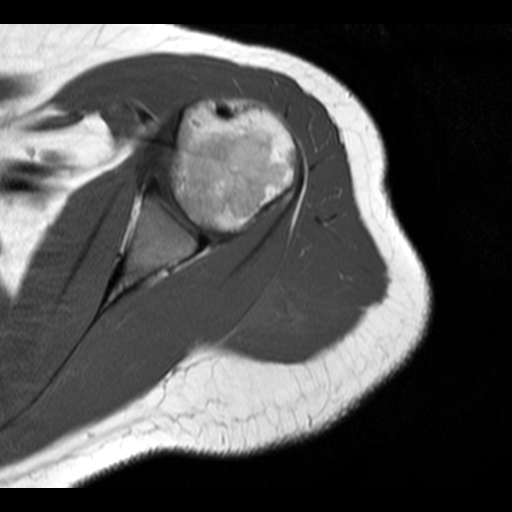
MRI of an extremity soft-tissue mass, one axial slice. Position 12 of 20 along the scan axis. 4 mm slice thickness. 512 × 512 image matrix, field of view 150 × 150 mm. Female patient. Case-level facts recorded for this patient, not image findings: histological type: malignant fibrous histiocytoma; grade: low; site of the primary tumour: left arm.
Structures marked on this image (expert manual segmentation):
- gross tumour volume (mass): box from (x=242, y=284) to (x=313, y=335) px